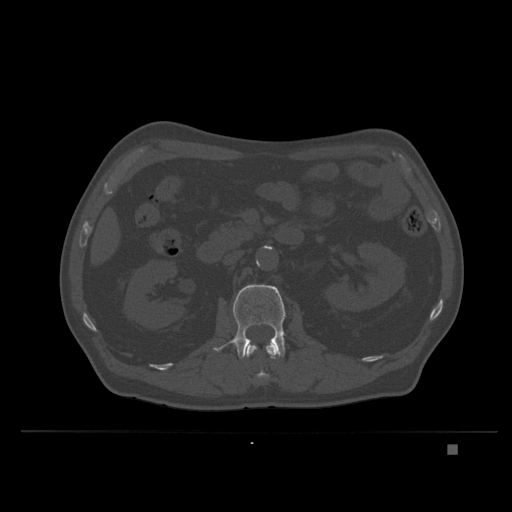
CT including the spine, one axial slice; slice 123 of 435 in the series (ordered by position); bone window (W 1800 / L 400 HU); 1.5 mm slice thickness; 512 × 512 image matrix. Male patient, age 73 years. Case-level facts recorded for this patient, not image findings: primary cancer: skin.
Structures marked on this image (semi-automatic segmentation, software-assisted and operator-edited):
- L1 vertebra: bounding box [x1, y1, x2, y2] px = [246, 341, 277, 382]
- L2 vertebra: [213, 284, 286, 359]